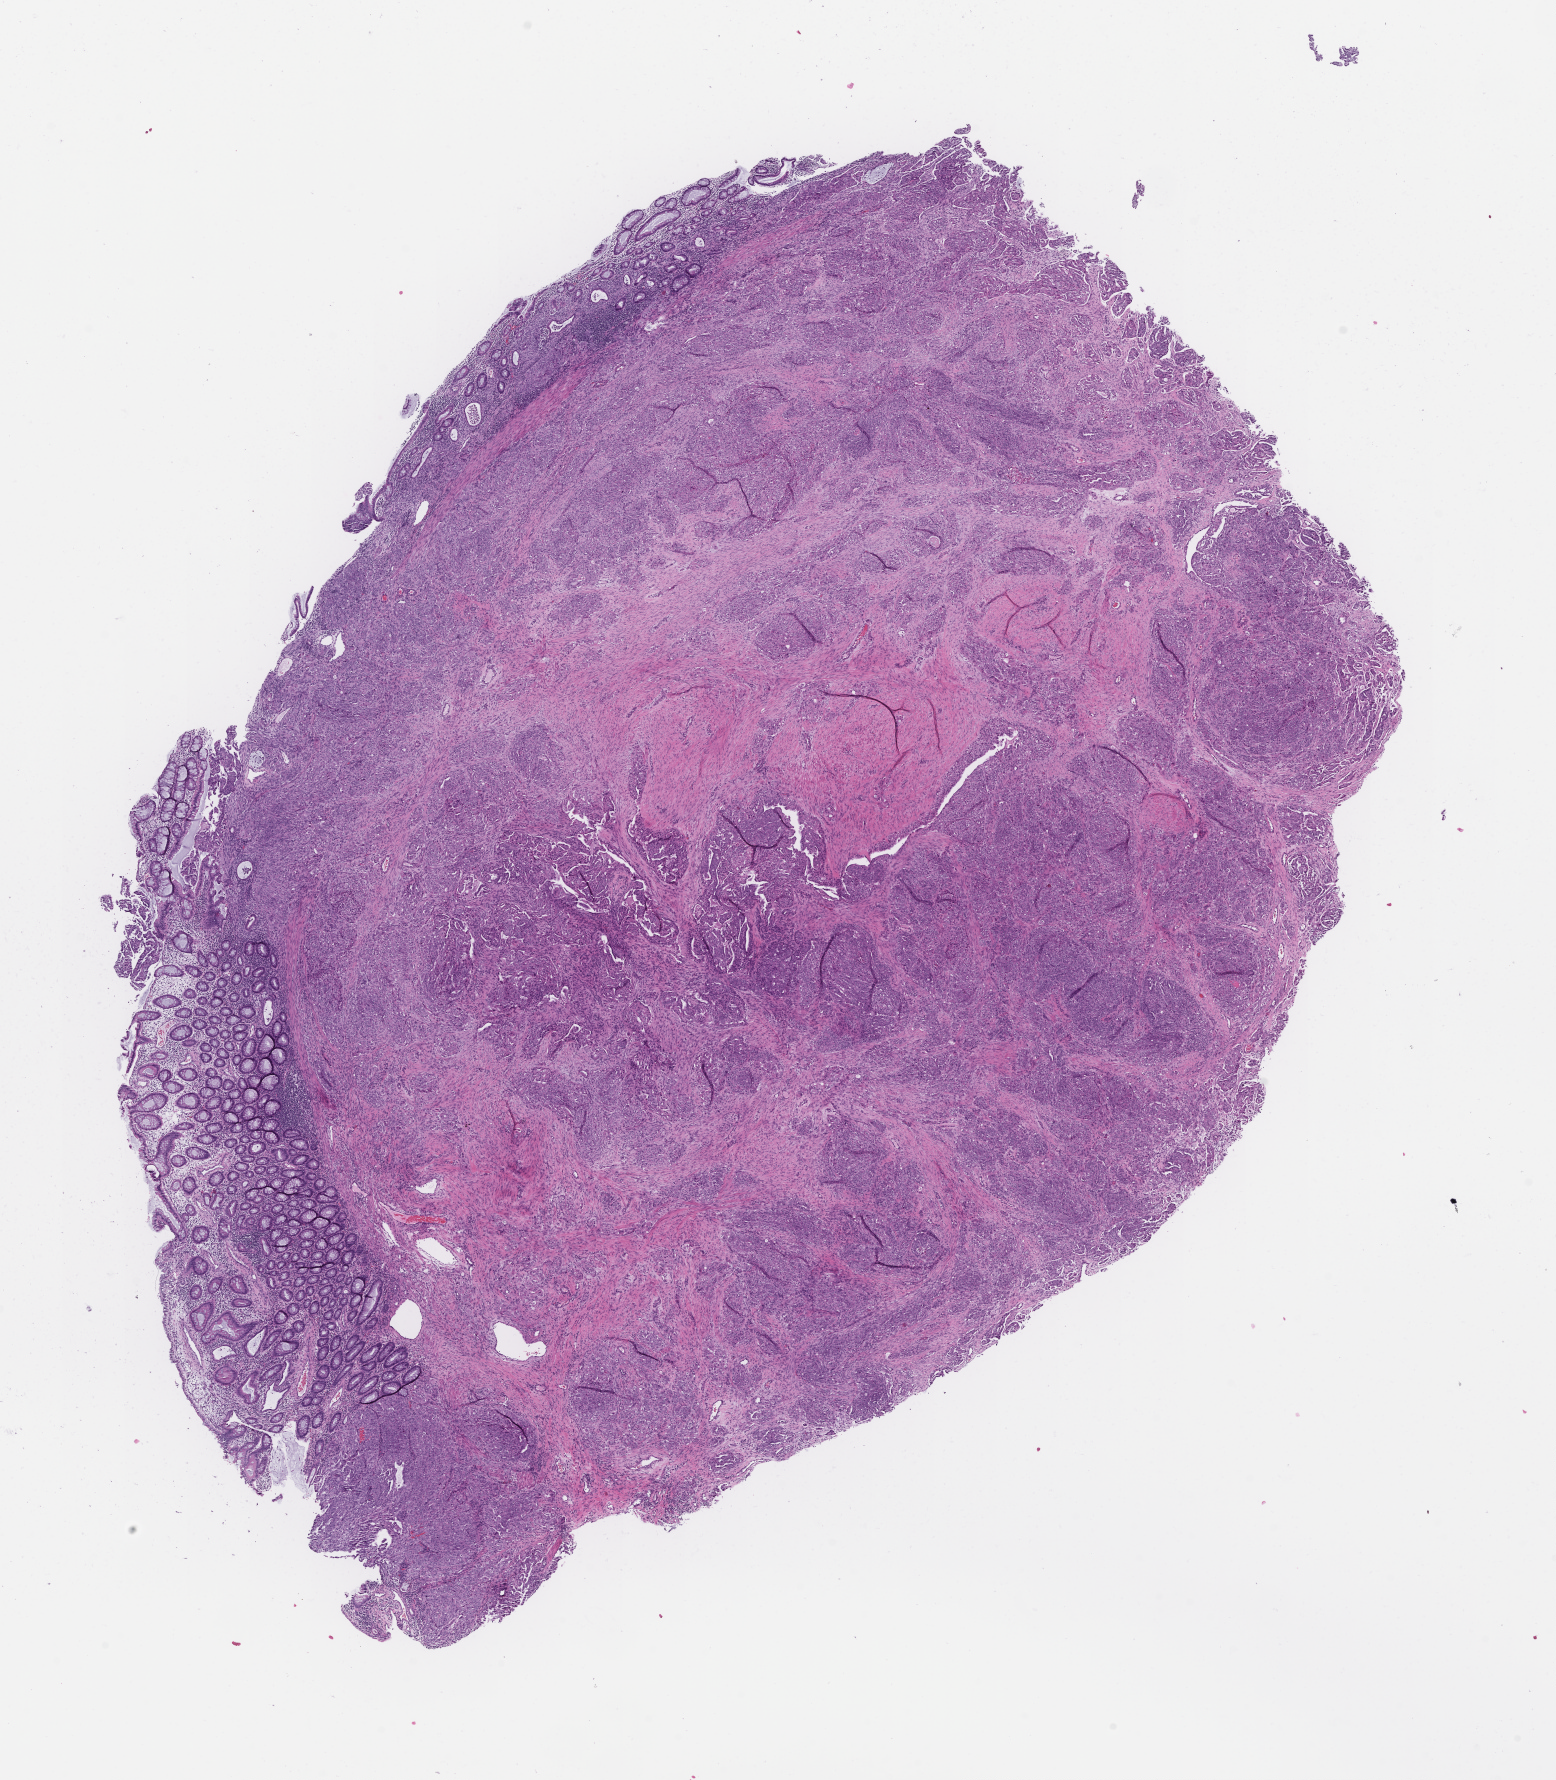
Whole-slide image, haematoxylin and eosin stain — shown as a low-resolution overview of the whole scanned area (about 12.6 x 14.4 mm); formalin-fixed paraffin-embedded section; specimen time point: collected at disease progression. Female patient.
This section: metastasis (sampled organ not recorded). Patient diagnosis (primary): Ovarian Carcinoma.